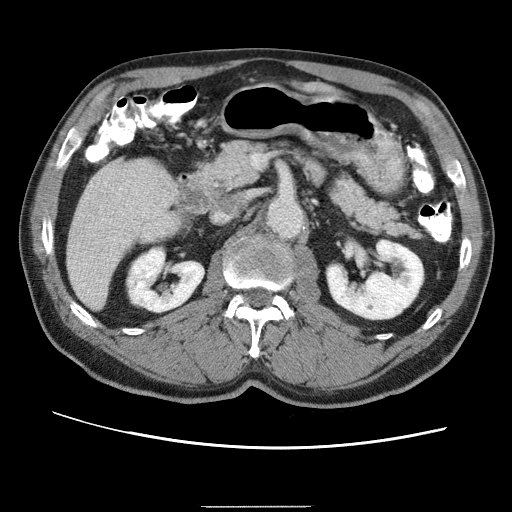
Contrast-enhanced abdominal CT (liver protocol), one axial slice; position 15 of 75 along the scan axis; reconstruction kernel STANDARD; 120 kVp; one of 2 acquisitions stored at this slice position; soft-tissue window (W 400 / L 40 HU); 2.5 mm slice thickness; 512 × 512 image matrix, field of view 360 × 360 mm. Case-level facts recorded for this patient, not image findings: diagnosis: hepatocellular carcinoma (patient treated with transarterial chemoembolisation; whether this scan precedes or follows treatment is not stated here); TNM stage (as recorded): Stage-II; Child-Pugh class: A; tumour differentiation: well differentiated; tumour size: 2 cm.
Structures marked on this image (semi-automatically segmented with operator editing):
- liver parenchyma outside the tumour (the mass and vessels are separate outlines, so this box may not span the whole liver): bounding box <66,162,162,304> (left, top, right, bottom; pixels)
- liver vessels: <100,165,127,230>